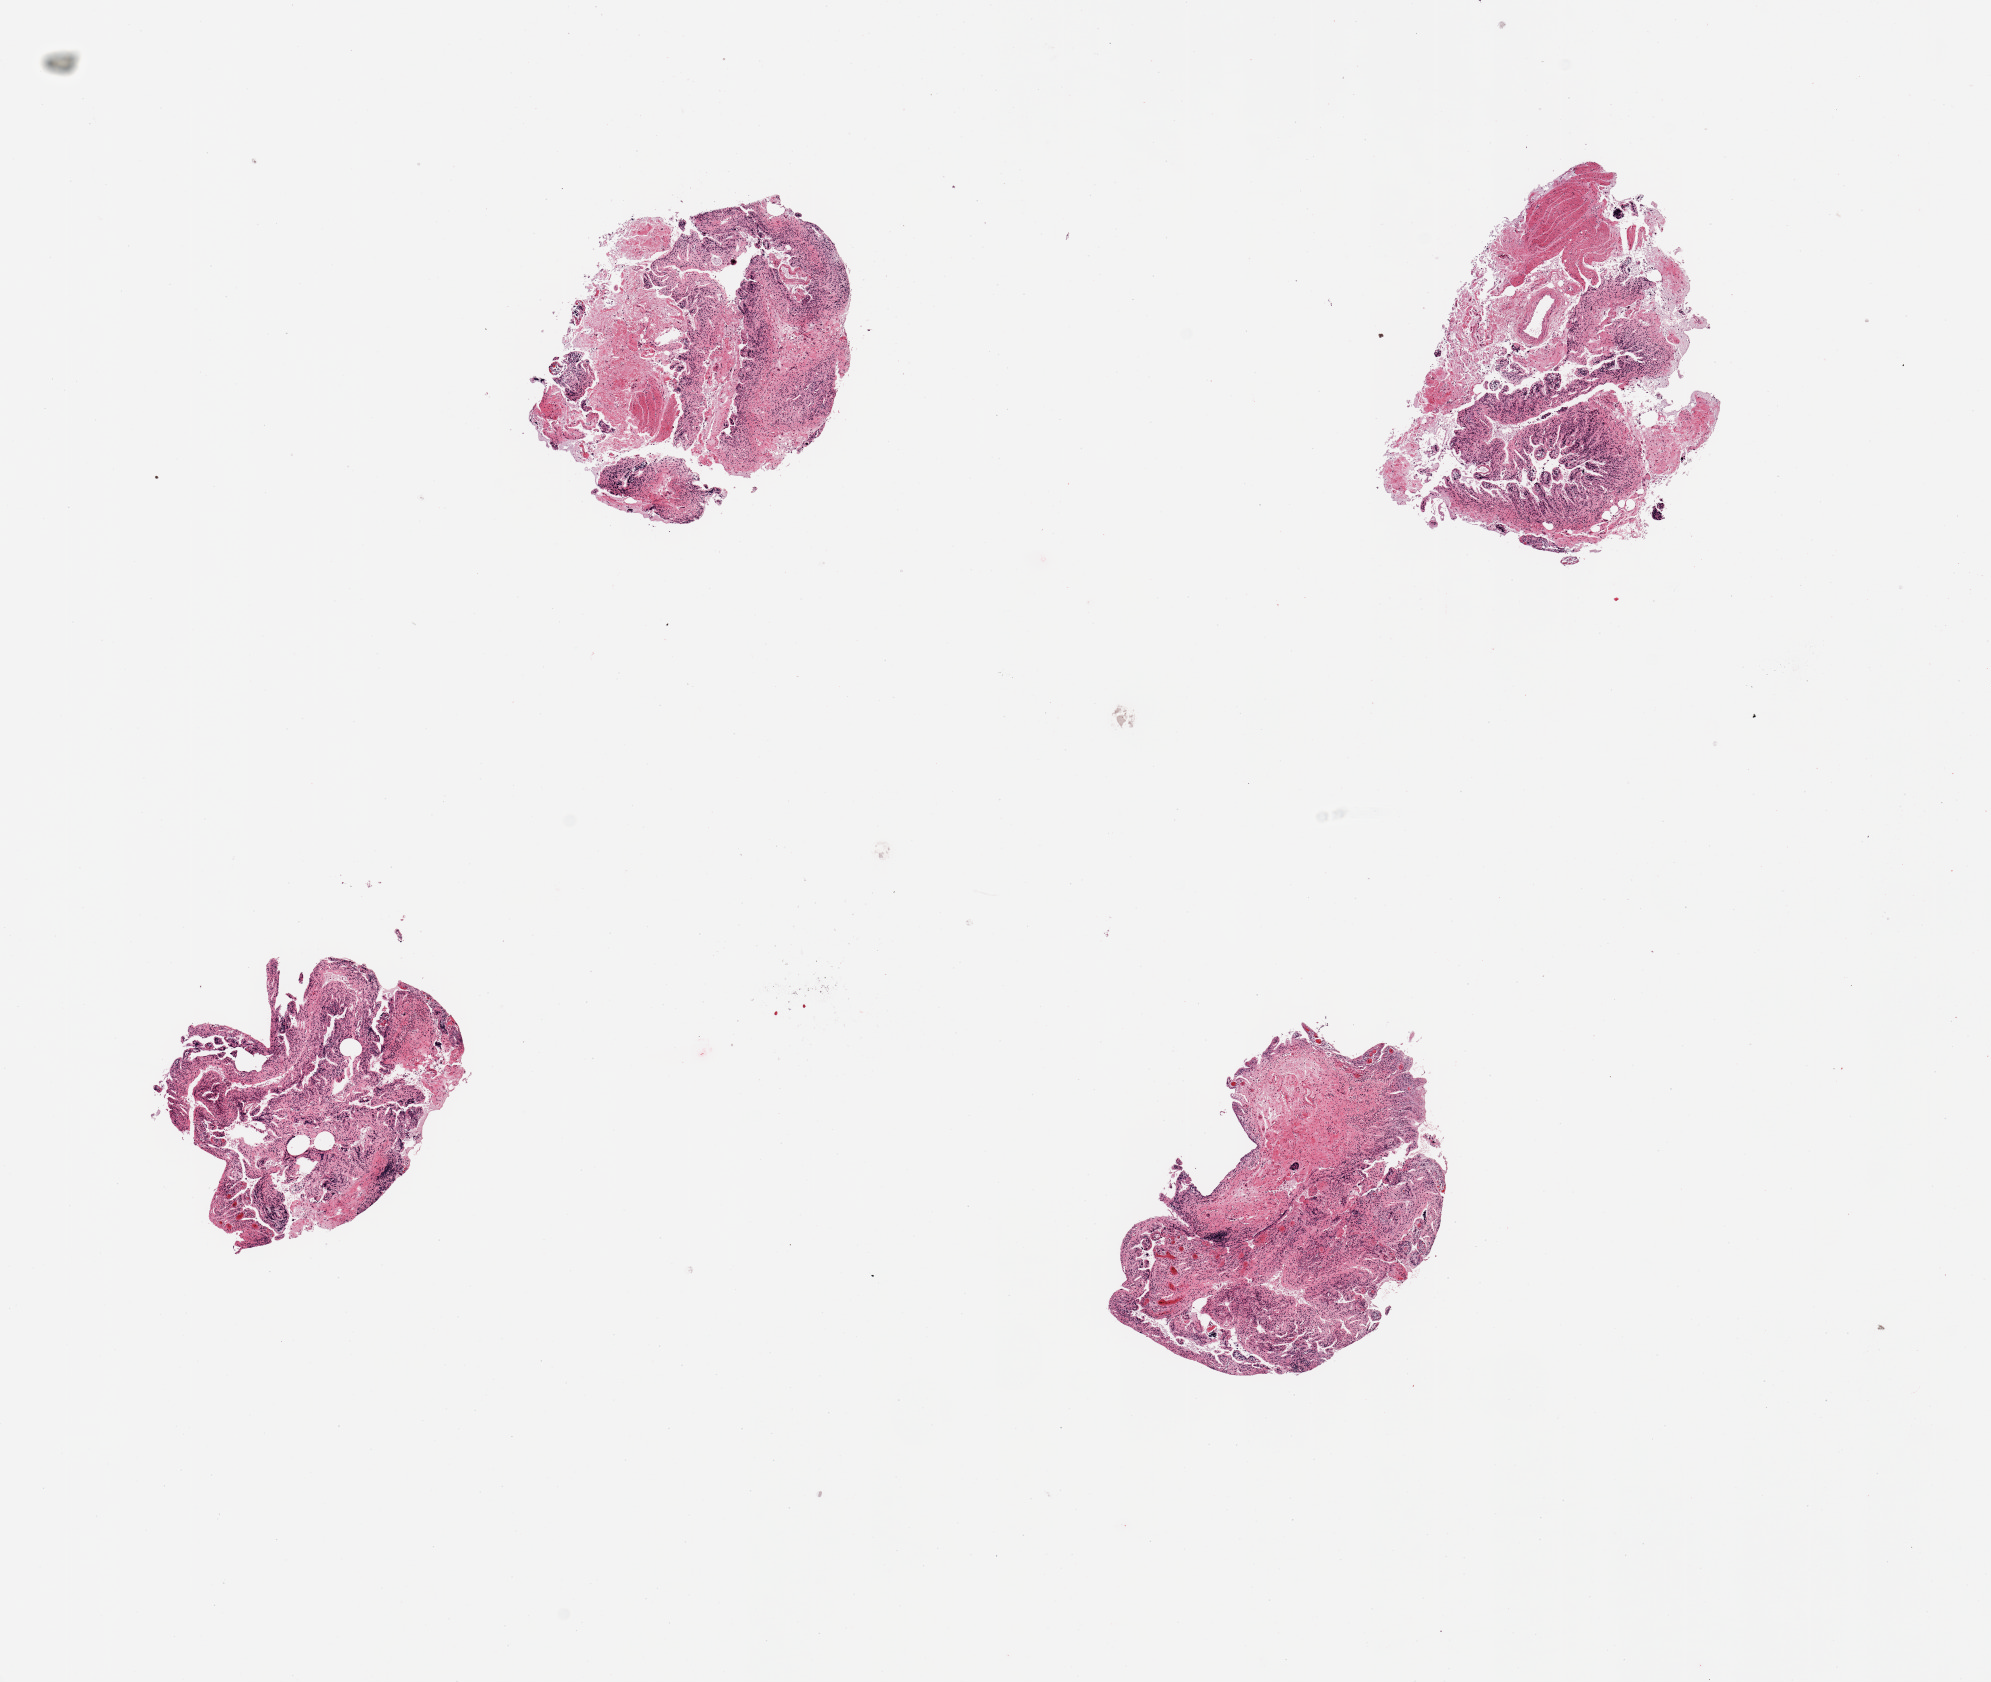
Whole-slide image, haematoxylin and eosin stain — shown as a low-resolution overview of the whole scanned area (about 15.8 x 13.3 mm). PAXgene-fixed, paraffin-embedded tissue. Section of ileum (target tissue). Donor tissue sample. Female donor.
Review note (as recorded): 4 pieces, totally autolyzed, insufficient lylmphoid aggregates to warrant analysis.